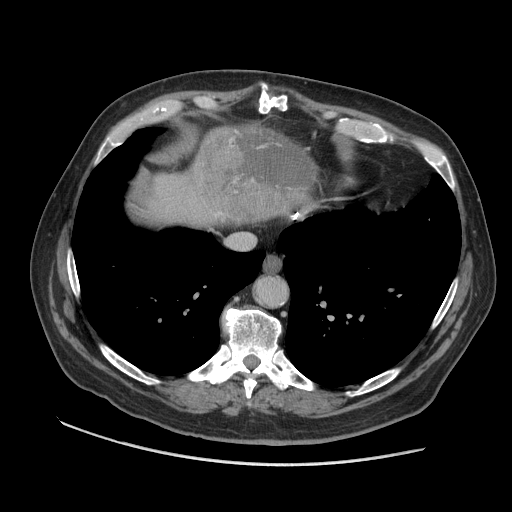
Contrast-enhanced abdominal CT (liver protocol), one axial slice; slice 92 of 109 in the series (ordered by position); reconstruction kernel STANDARD; soft-tissue window (W 400 / L 40 HU); 512 × 512 image matrix, field of view 420 × 420 mm. Case-level facts recorded for this patient, not image findings: diagnosis: hepatocellular carcinoma (patient treated with transarterial chemoembolisation; whether this scan precedes or follows treatment is not stated here); TNM stage (as recorded): Stage-I; Child-Pugh class: A; tumour nodularity: uninodular.
Outlined on this slice (semi-automatic segmentation, software-assisted and operator-edited):
- liver parenchyma outside the tumour (the mass and vessels are separate outlines, so this box may not span the whole liver): box from (x=132, y=126) to (x=275, y=224) px
- mass: (x=191, y=120)–(x=318, y=224)